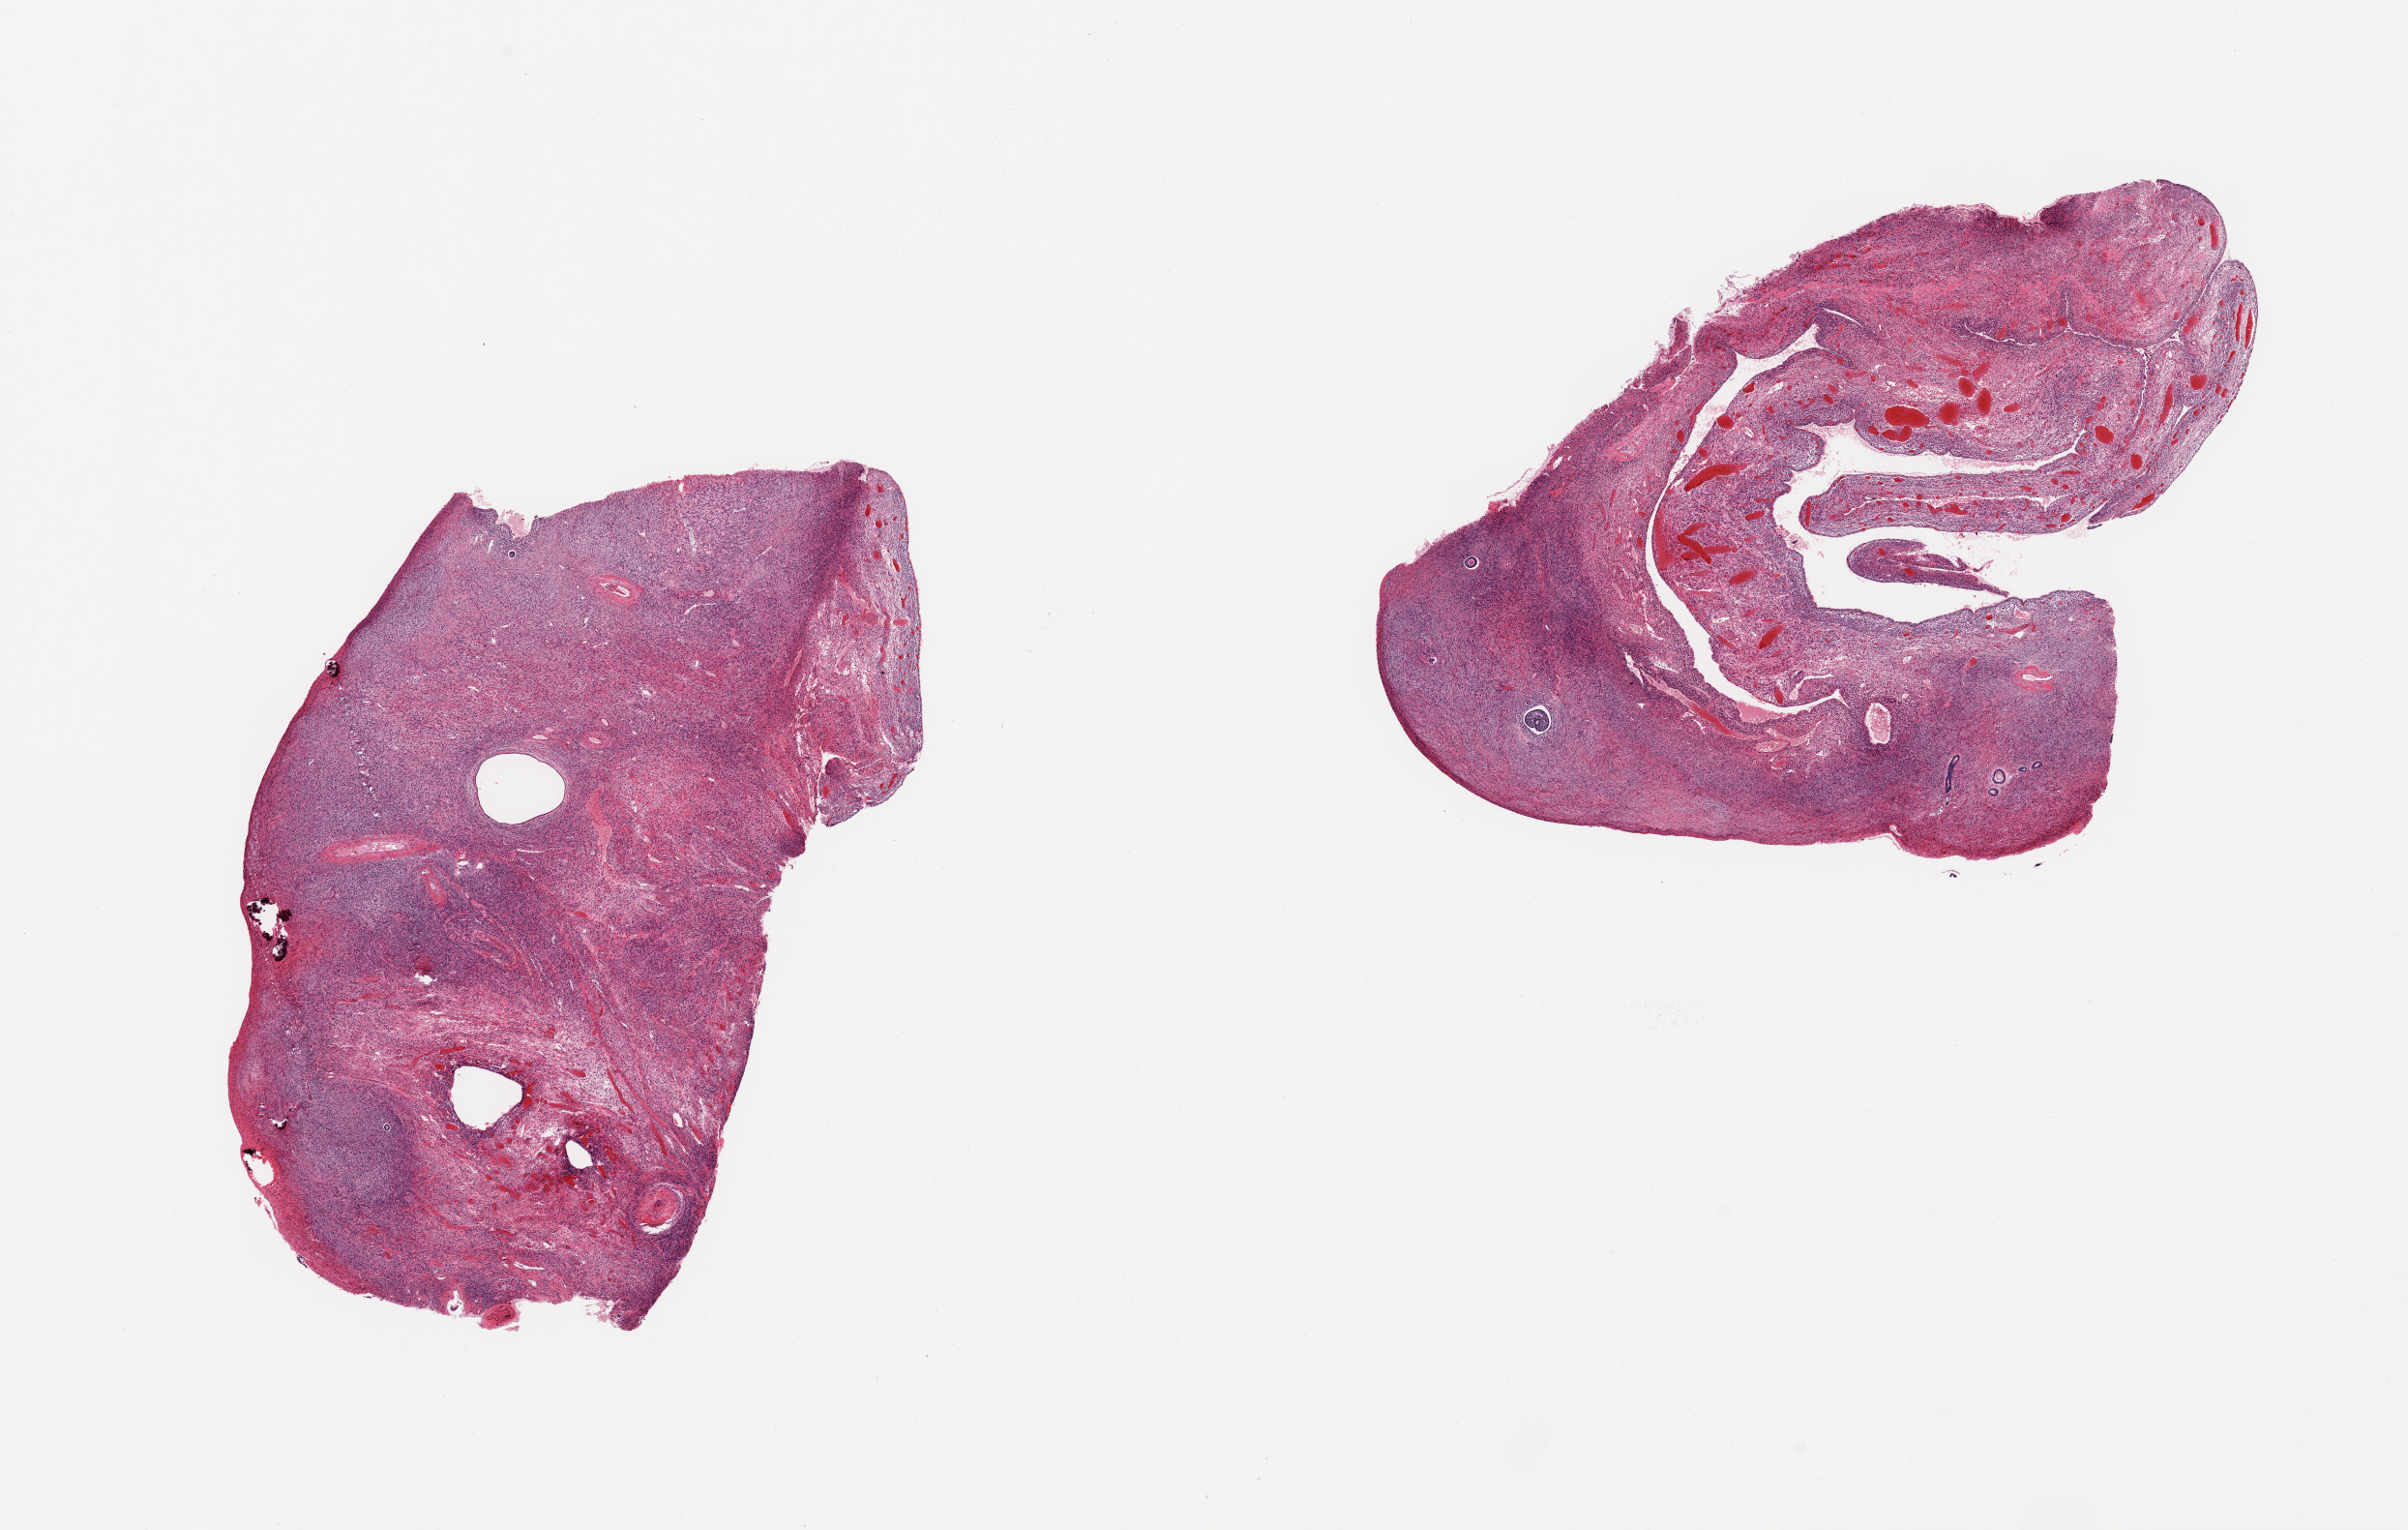
Whole-slide image, haematoxylin and eosin stain, brightfield, whole scanned area (about 19.7 x 12.5 mm) shown as a low-resolution overview, PAXgene-fixed, paraffin-embedded tissue, sampled site (target tissue): ovary, donor tissue sample. Donor sex: female.
Reviewer comment on this tissue sample: 2 pieces; few follicles and inclusion glands, focal calcifications.